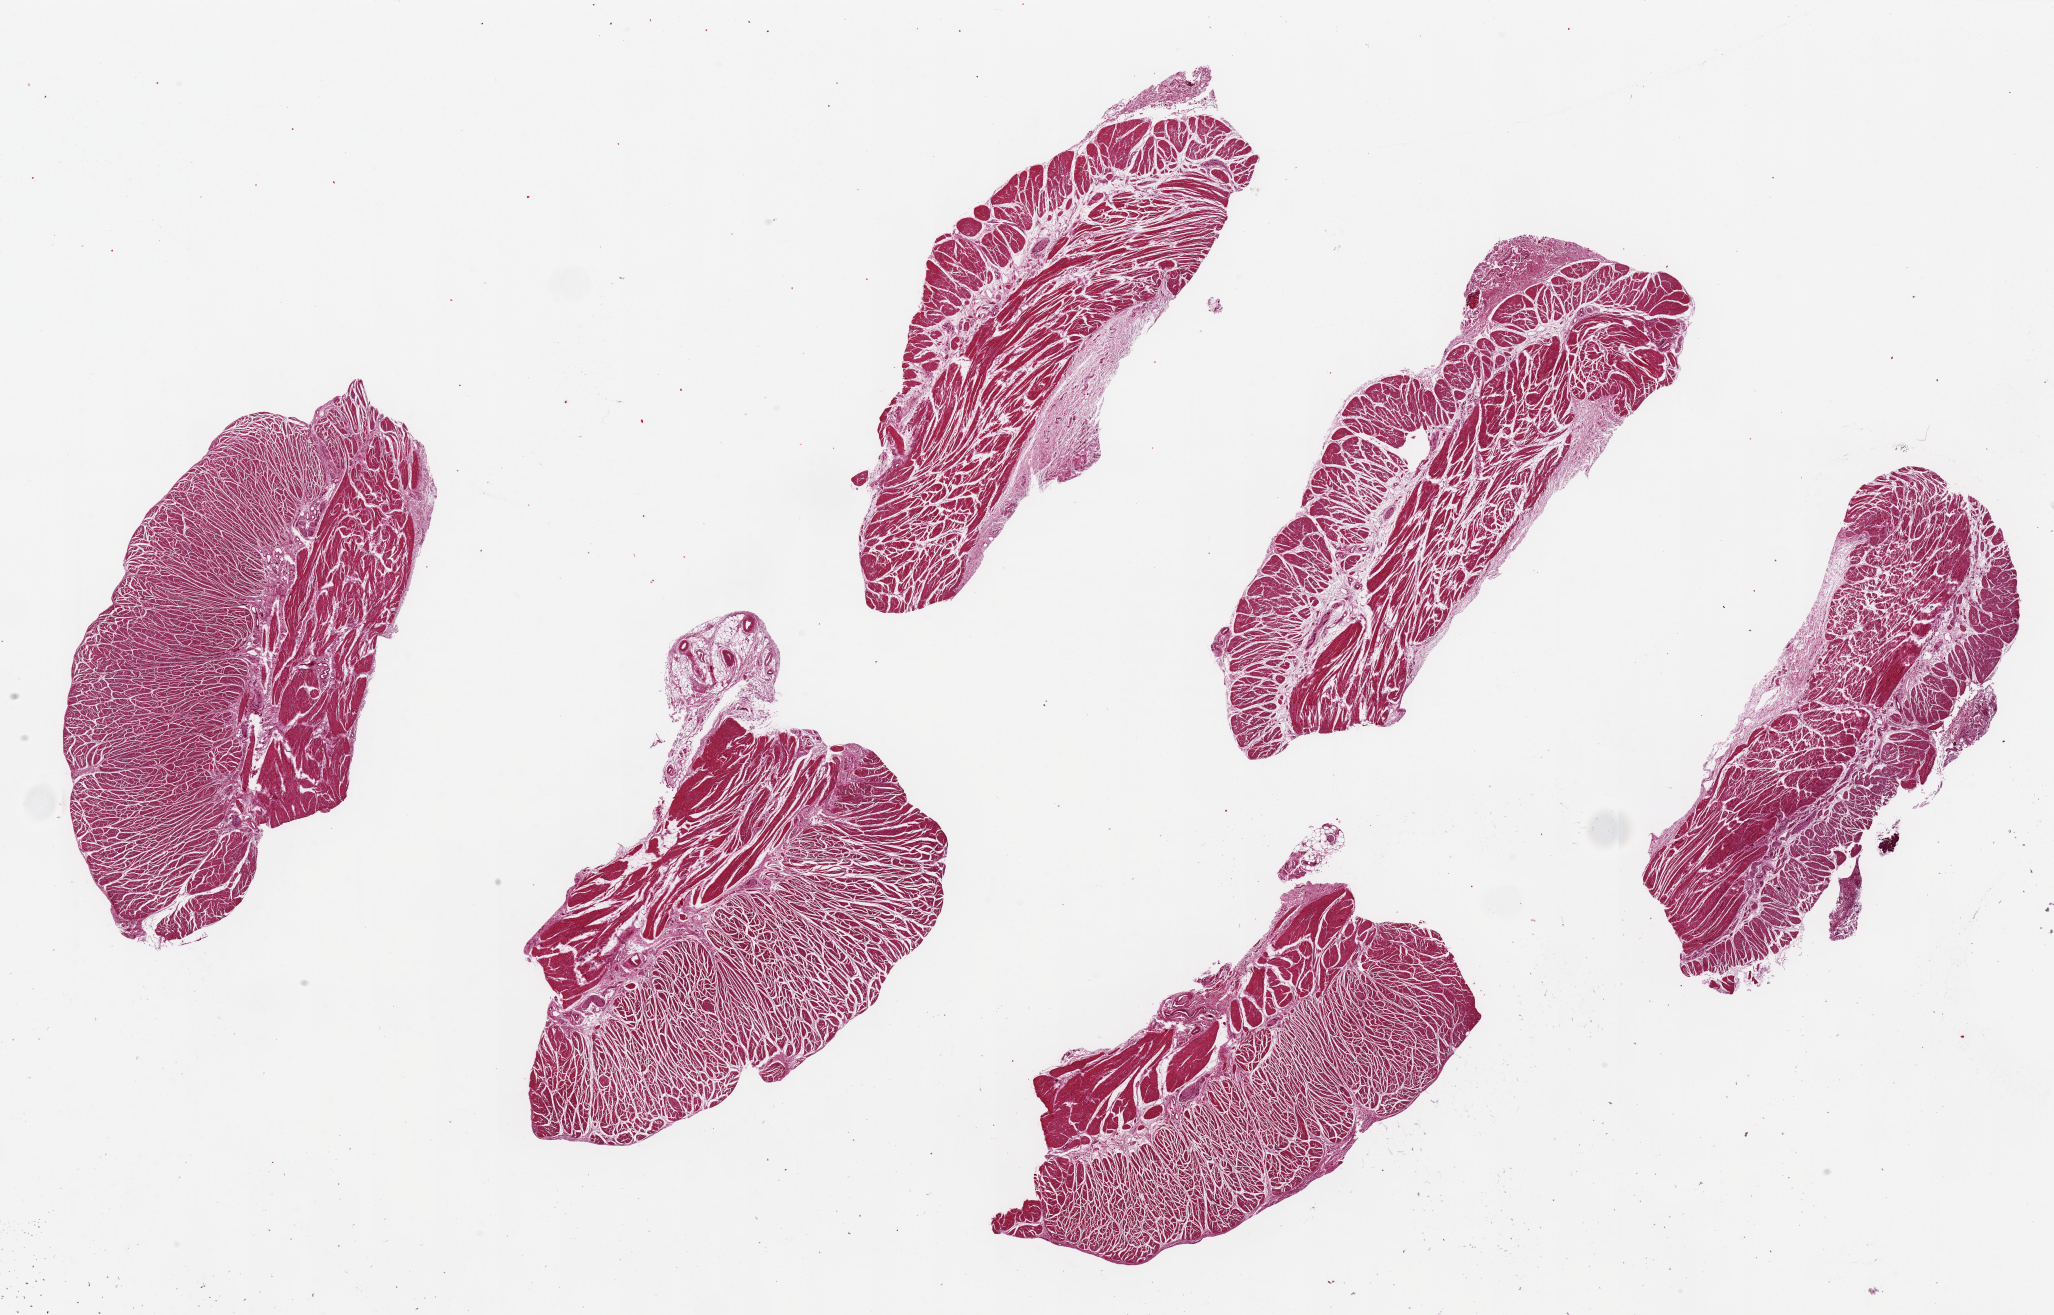
Whole-slide image, haematoxylin and eosin stain, brightfield — whole scanned area (about 32.5 x 20.8 mm) shown as a low-resolution overview; PAXgene-fixed paraffin-embedded (PFPE) section; section of esophageal muscle (target tissue); tissue donor sample. Donor: female.
* pathologist's review note for this sample: 6 pieces, ~9x3mm